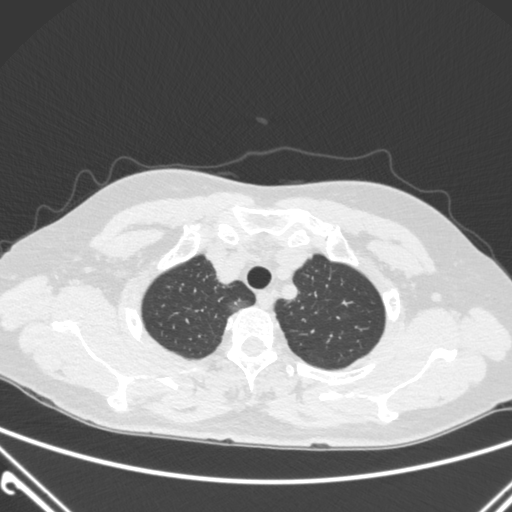
Chest CT, one axial slice. Position 245 of 300 along the scan axis. 120 kVp. Lung window (W 1500 / L -600 HU). 1 mm slice thickness. 512 × 512 image matrix, field of view 350 × 350 mm. Patient: female, 54 years. From the clinical record (not read from this slice): clinical TNM (as recorded): T1a N0 M0; histopathological grade: G1.
Annotated regions visible in this slice (rectangle marked by the reading radiologist):
- lung tumour (recorded histology: adenocarcinoma): box from (x=222, y=293) to (x=253, y=316) px